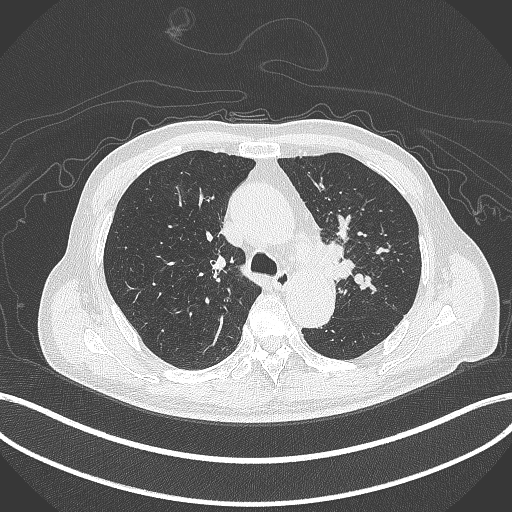
Chest CT, one axial slice; position 301 of 417 along the scan axis; lung window (W 1500 / L -600 HU); 1 mm slice thickness; 512 × 512 image matrix. Patient: male, 77 years. Case-level facts recorded for this patient, not image findings: clinical TNM (as recorded): T3 N1 M0.
Annotated regions visible in this slice (bounding box drawn by a radiologist):
- lung tumour (recorded histology: adenocarcinoma): box from (x=321, y=240) to (x=359, y=289) px